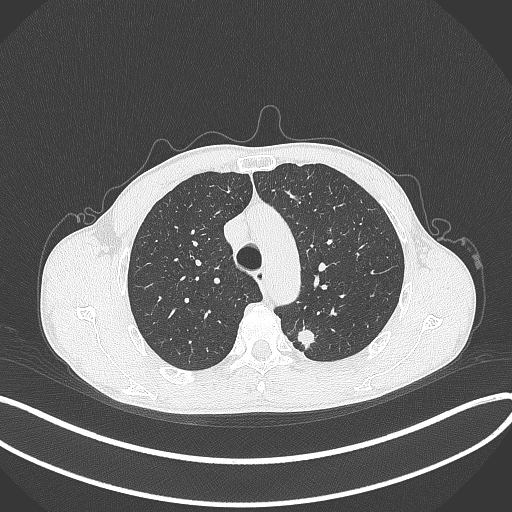
Chest CT, one axial slice. Slice 298 of 429 in the series (ordered by position). Reconstruction kernel B70f. 120 kVp. Lung window (W 1500 / L -600 HU). 512 × 512 image matrix, field of view 400 × 400 mm. Male patient, age 51 years. Case-level facts recorded for this patient, not image findings: clinical TNM (as recorded): T2a N1 M1.
Annotated regions visible in this slice (bounding box drawn by a radiologist):
- lung tumour (recorded histology: adenocarcinoma): box from (x=292, y=319) to (x=320, y=353) px